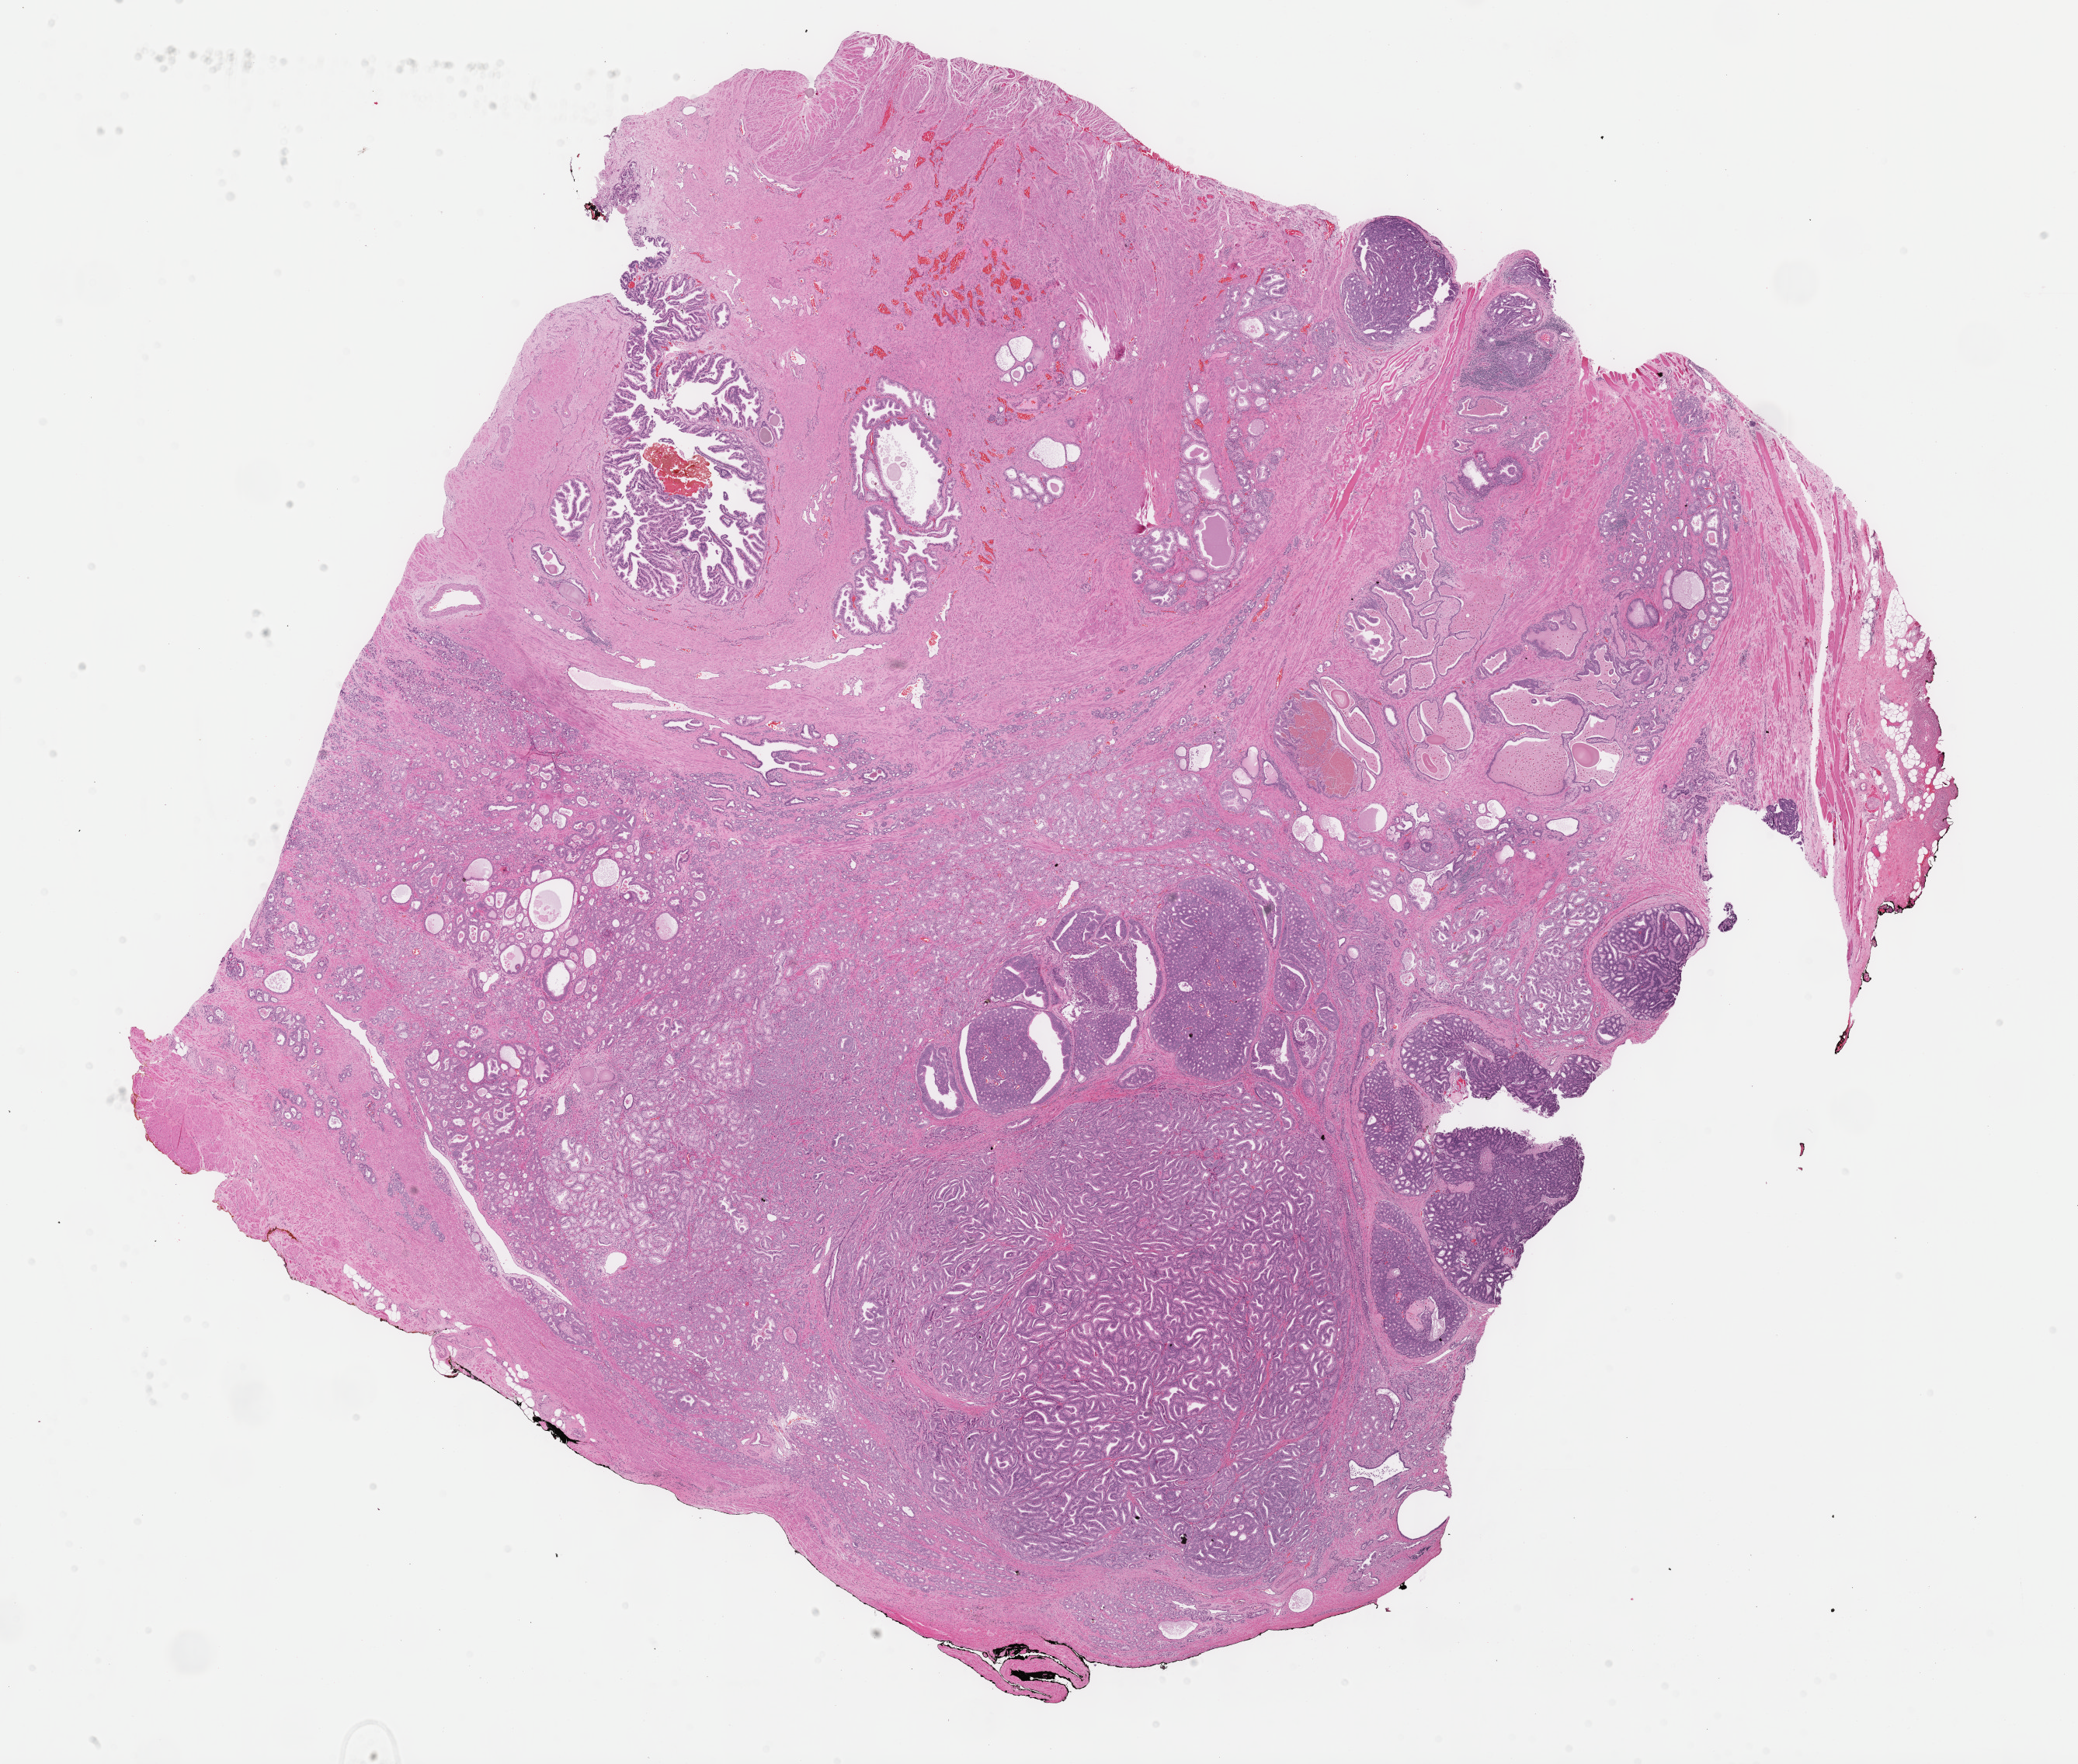
Digitized H&E tissue section (whole slide) — a low-resolution overview of the entire scanned area, about 21.6 x 18.4 mm (acquisition: 40x scan); formalin-fixed paraffin-embedded (FFPE) diagnostic section; primary tumour sample from the prostate. Male, age 51 years at initial diagnosis. Gleason score: 7 (4+3).
Lymph nodes positive (case pathology): 0 of 4 examined. Diagnosis: Adenocarcinoma, NOS (prostate gland).